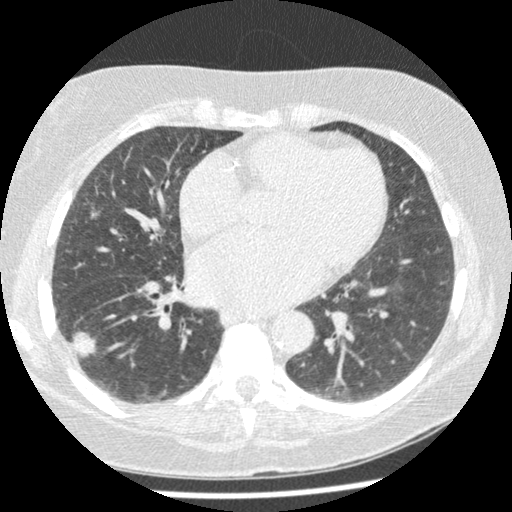
Low-dose screening chest CT, one axial slice. Position 109 of 241 along the scan axis. 120 kVp. Lung window (W 1500 / L -600 HU). 512 × 512 image matrix, field of view 305 × 305 mm.
Annotated regions visible in this slice (manually delineated by an expert):
- lesion 1 (tumor, lower lobe of right lung): bounding box (x1, y1, x2, y2) in pixels: (72, 331, 96, 358)